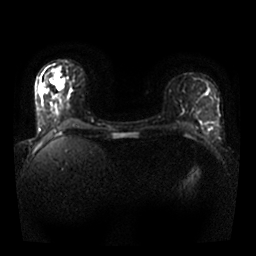
Breast MRI, one axial slice. Diffusion-weighted series; image 2 of 4 stored at this slice position (different b-values; order by instance number). 1.5 T. 256 × 256 image matrix, field of view 330 × 330 mm. Female patient.
Annotated regions visible in this slice (manually delineated by an expert):
- tumour on diffusion-weighted imaging: bounding box (x1, y1, x2, y2) in pixels: (51, 73, 64, 89)